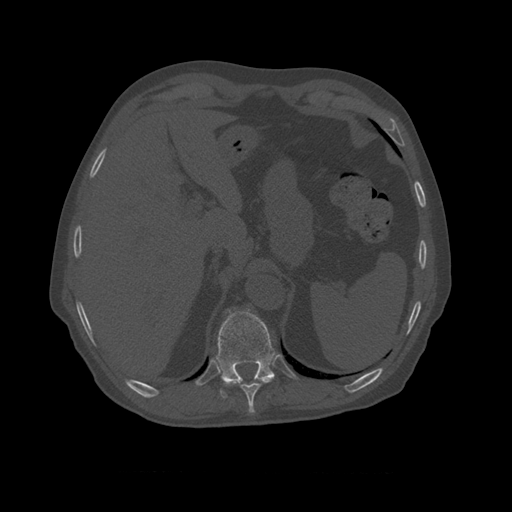
CT including the spine, one axial slice; 120 kVp; bone window (W 1800 / L 400 HU); 1.25 mm slice thickness; 512 × 512 image matrix, field of view 405 × 405 mm. Patient age 75 years. Case-level facts recorded for this patient, not image findings: primary cancer: prostate.
Annotated regions visible in this slice (semi-automatically segmented with operator editing):
- T10 vertebra: box from (x=216, y=309) to (x=275, y=399) px
- T9 vertebra: (x=227, y=380)–(x=271, y=410)